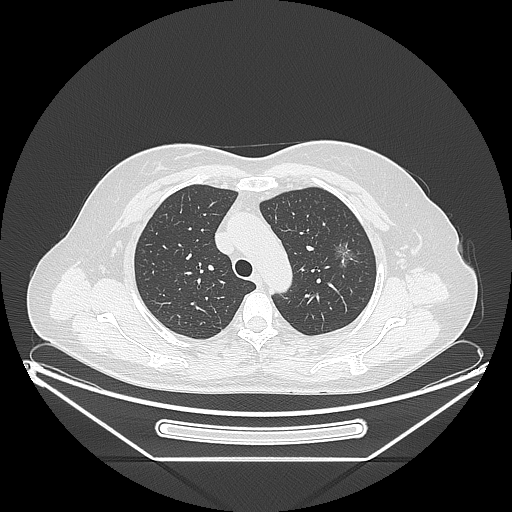
Chest CT, one axial slice. Position 164 of 226 along the scan axis. 120 kVp. Lung window (W 1500 / L -600 HU). 1.25 mm slice thickness. 512 × 512 image matrix, field of view 447 × 447 mm. Female patient, age 54 years. From the clinical record (not read from this slice): clinical TNM (as recorded): T1c N0 M0; histopathological grade: G1.
Annotated regions visible in this slice (rectangle marked by the reading radiologist):
- lung tumour (recorded histology: adenocarcinoma): bounding box [x1, y1, x2, y2] px = [330, 234, 360, 272]